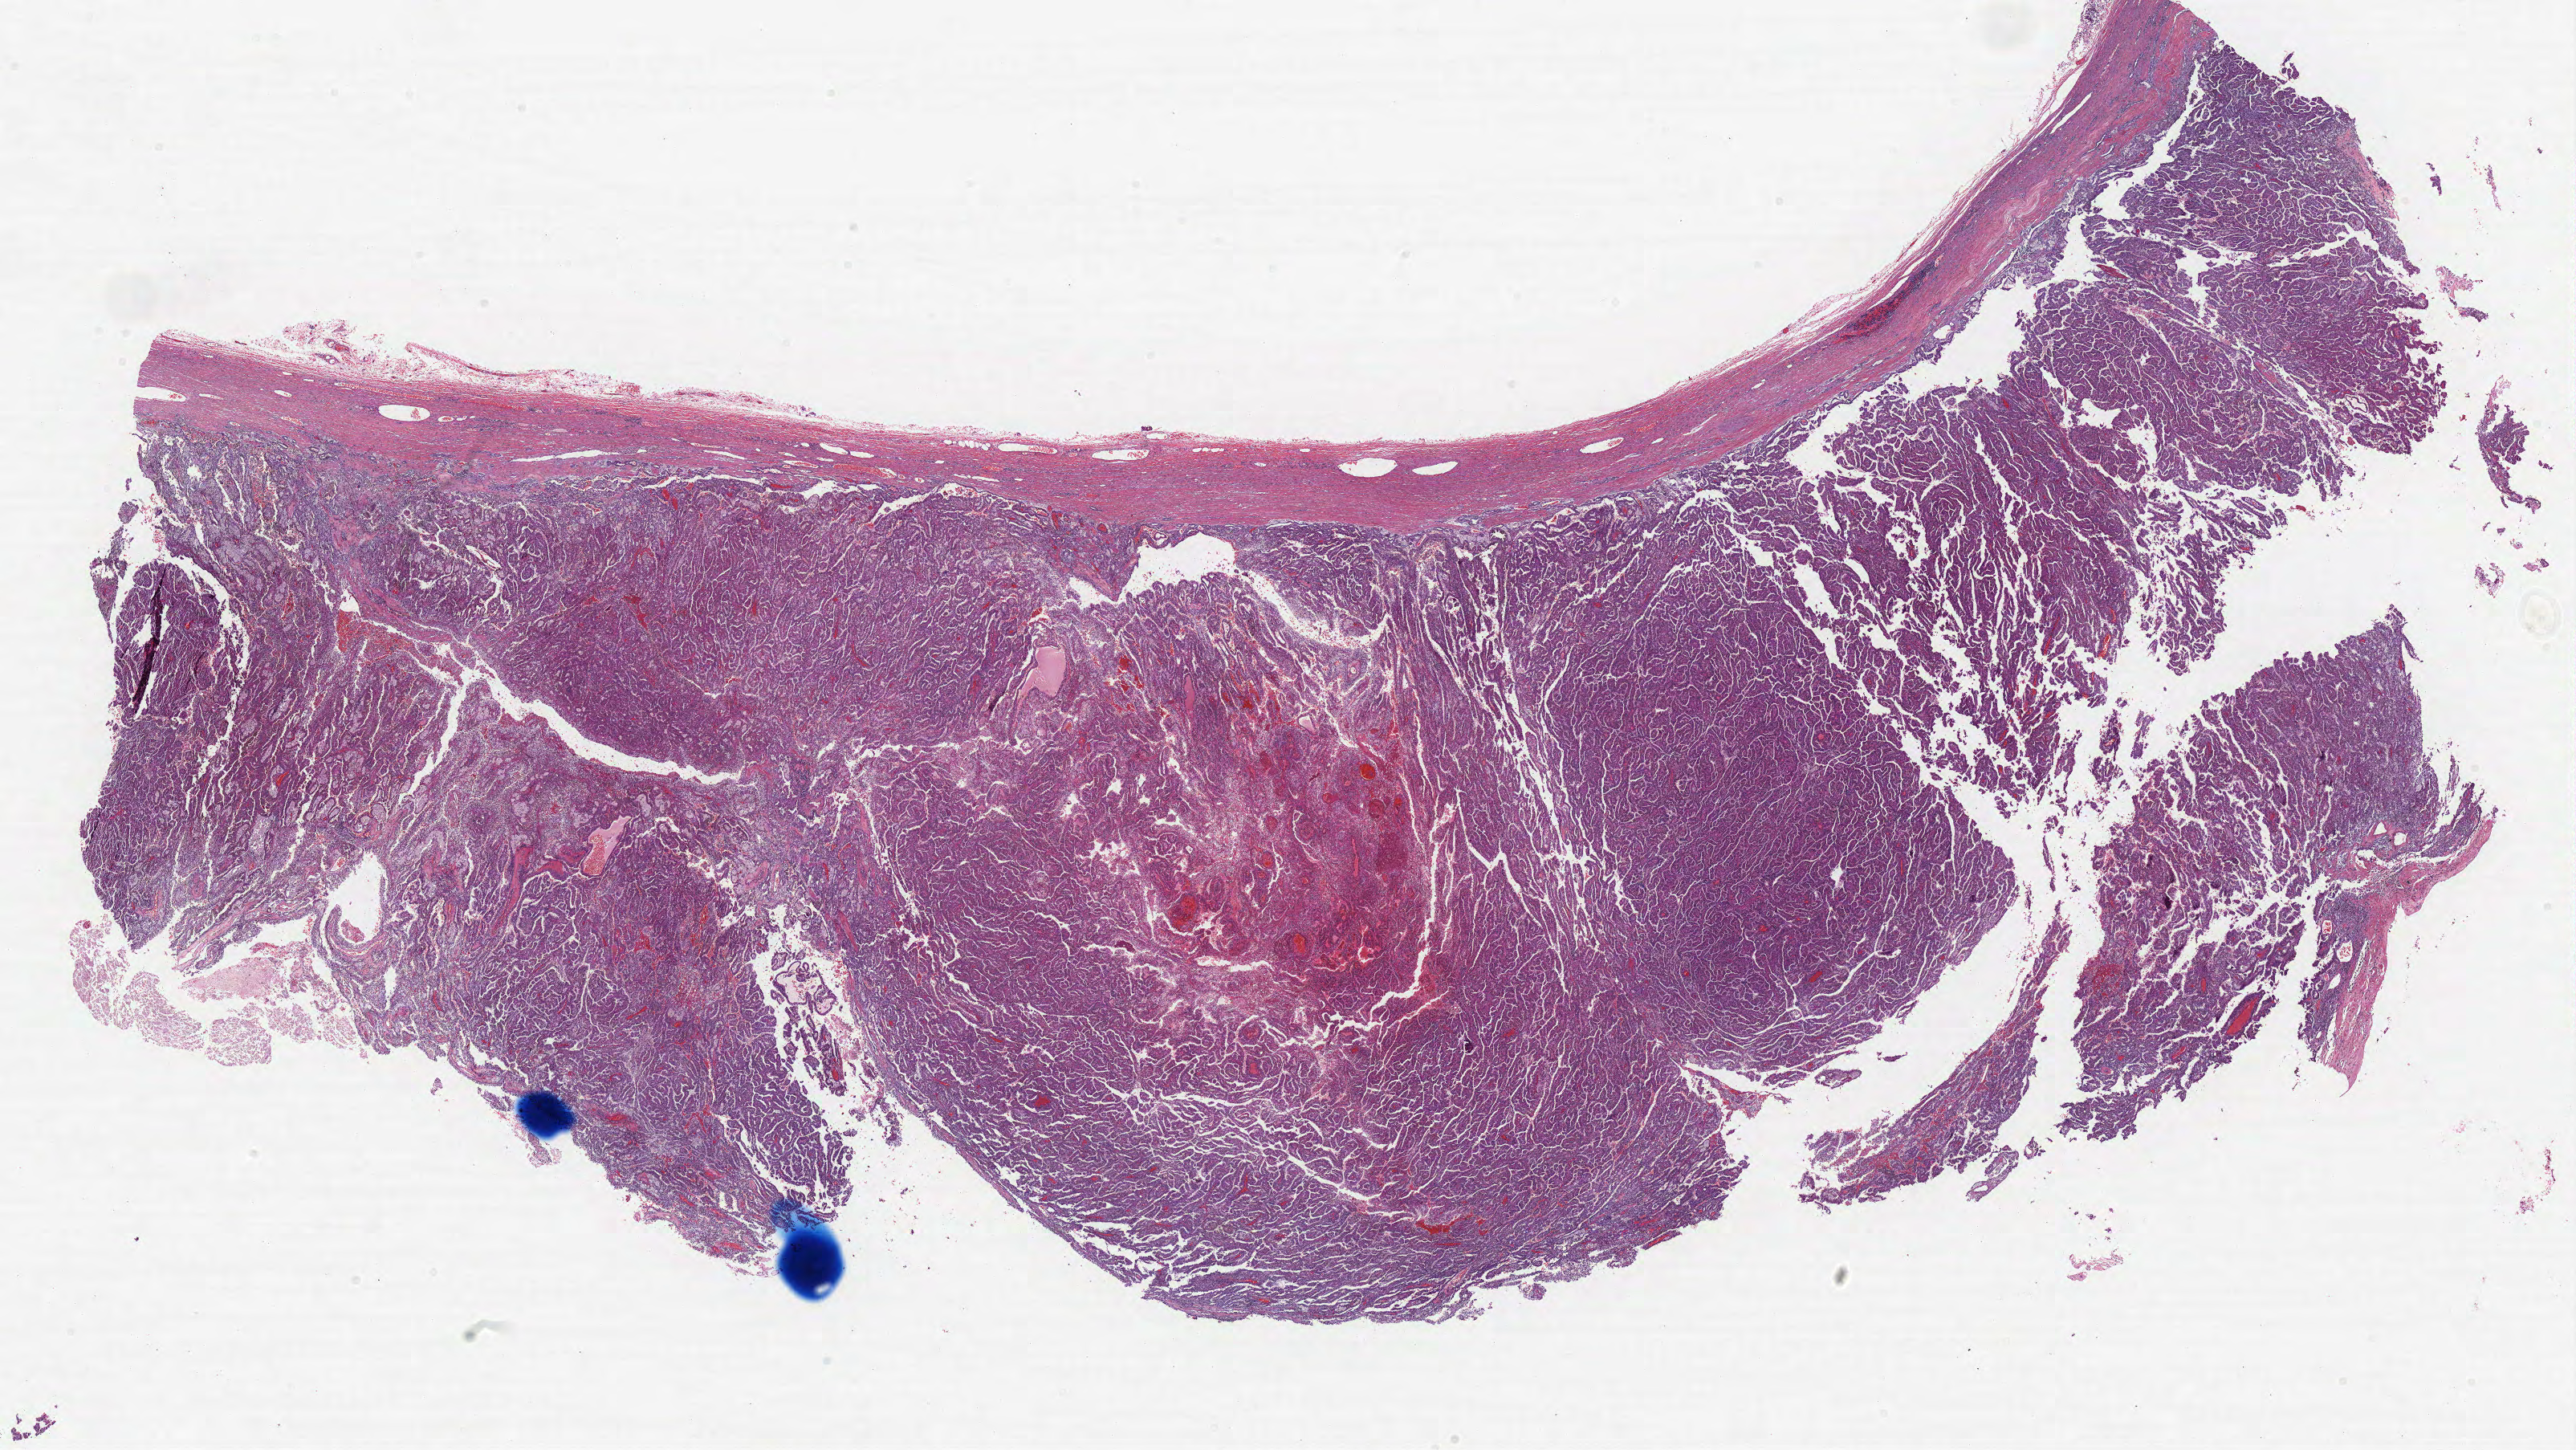
H&E-stained whole-slide image — whole scanned area (about 25.7 x 14.4 mm, slide scanned at 40x) shown as a low-resolution overview. Formalin-fixed paraffin-embedded (FFPE) diagnostic section. Kidney, primary tumour sample. Male patient; age at initial diagnosis 74 years.
AJCC pathologic stage: II (6th edition). Diagnosis: Papillary adenocarcinoma, NOS. TNM: T2 N0 M0. Laterality: right.